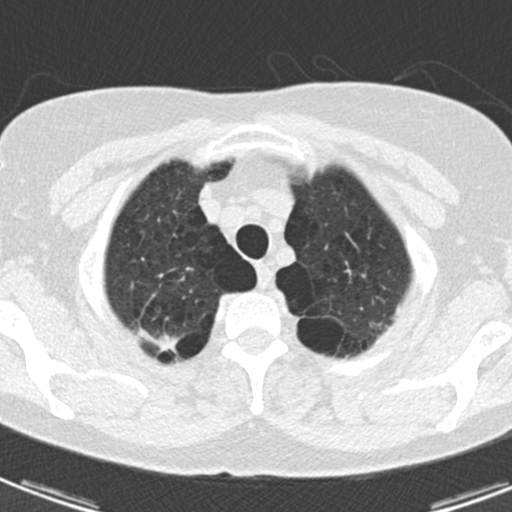
Axial slice from a low-dose chest CT screening exam. Third screening round (two years after baseline). Lung window (W 1500 / L -600 HU). Slice 20 of 174 in the series. 512 × 512 image matrix, field of view 281 × 281 mm. Female, age 59 years at enrolment.
Expert reader's lesion annotation, box from (x=131, y=320) to (x=187, y=364) px. Reader record for this screening exam (exam-level; its link to the box is not recorded): non-calcified nodule or mass ≥4 mm, right upper lobe, 12 × 7 mm, spiculated (stellate) margins, soft tissue attenuation, pre-existing on the prior screen: yes; interval growth: yes. Later outcome: lung cancer diagnosed 32 days after this screen — adenocarcinoma, NOS, right upper lobe, poorly differentiated (G3), stage IA (AJCC 6th edition), 20 mm at pathology.